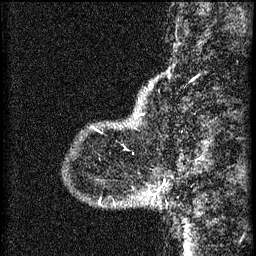
Breast MRI (dynamic contrast-enhanced), one sagittal slice. Slice 8 of 60 in the series (ordered by position). 3 images stored at this slice position (order not interpretable as contrast timing). 1.5 T. TE 4.2 ms, TR 8.2 ms. 256 × 256 image matrix, field of view 180 × 180 mm. Patient: female, 37 years.
Annotated regions visible in this slice (semi-automatically segmented with operator editing):
- analysis volume of interest (the breast-tissue region the enhancement analysis was run in; not a lesion): bounding box (x1, y1, x2, y2) in pixels: (137, 182, 165, 205)
- tumour enhancement mask (voxels above the 70 % enhancement threshold inside the analysis volume of interest): (163, 182, 165, 185)